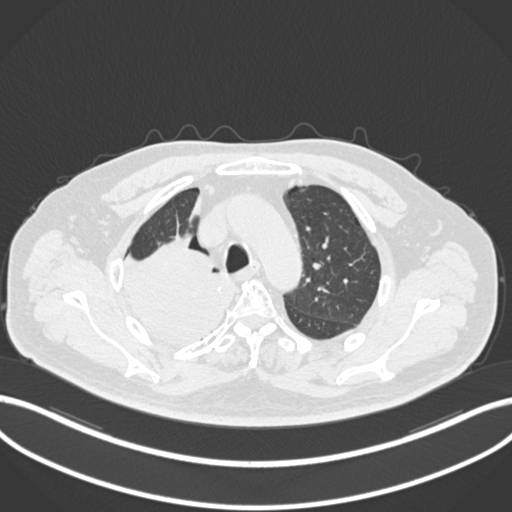
Chest CT, one axial slice; position 159 of 218 along the scan axis; lung window (W 1500 / L -600 HU); 1 mm slice thickness; 512 × 512 image matrix, field of view 400 × 400 mm. Male patient, age 68 years. Case-level facts recorded for this patient, not image findings: clinical TNM (as recorded): T2a N0 M0.
Structures marked on this image (rectangle marked by the reading radiologist):
- lung tumour (recorded histology: adenocarcinoma): bounding box <118,238,237,343> (left, top, right, bottom; pixels)